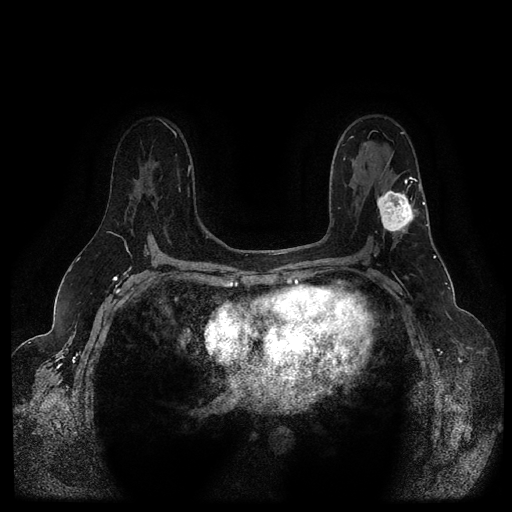
Breast MRI (dynamic contrast-enhanced, multi-phase), one axial slice. Slice 64 of 116 in the series (ordered by position). Dynamic contrast-enhanced series, time point 2 of 5 at this slice position (early post-contrast). 1.5 T. TE 2.6 ms, TR 5.3 ms. 2 mm slice thickness. 512 × 512 image matrix. Patient: female, 54 years.
Outlined on this slice (semi-automatic segmentation, software-assisted and operator-edited):
- breast lesion (labelled 'tumour' in the annotation; benign lesions carry a separate 'benign' label): bounding box (x1, y1, x2, y2) in pixels: (375, 189, 419, 239)